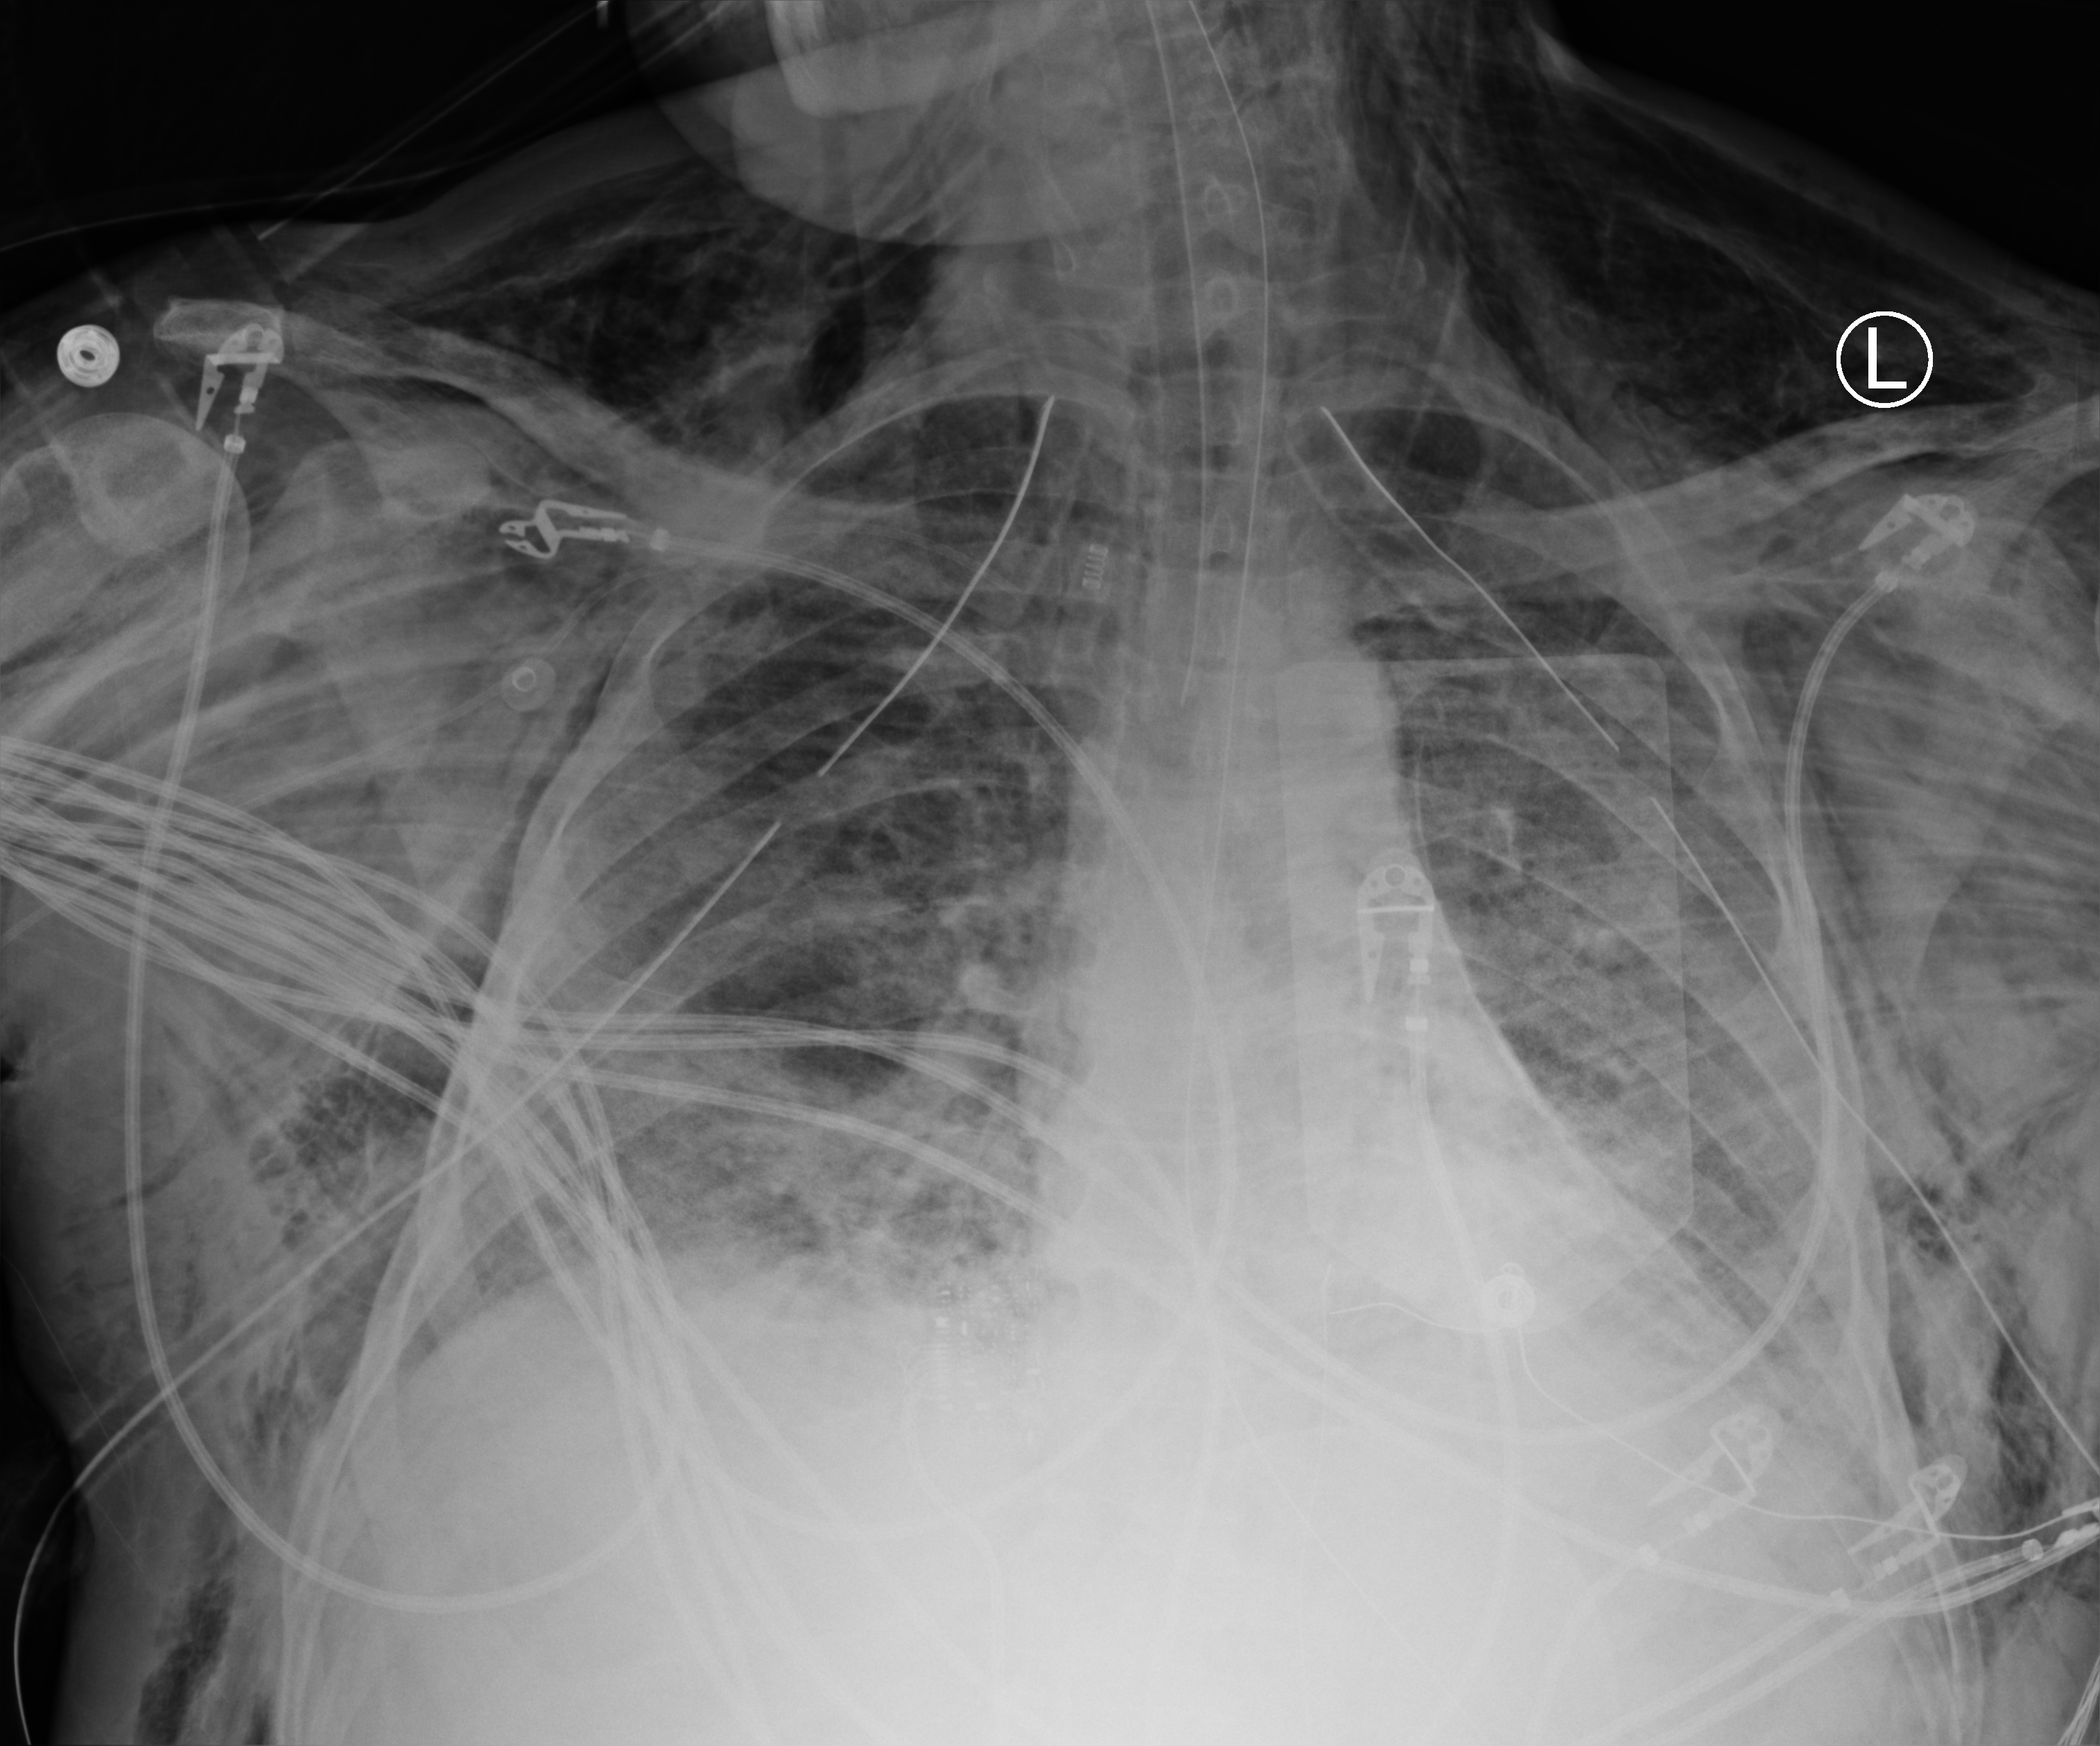
Bedside chest radiograph (computed radiography), anteroposterior (AP) projection. Patient hospitalised with COVID-19; male, aged 18–59 years.
Admission-level facts for this patient (not findings on this image; timing relative to this image not recorded): diabetes (admission record): no.